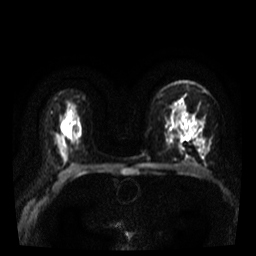
Breast MRI, one axial slice. Diffusion-weighted series; image 2 of 4 stored at this slice position (different b-values; order by instance number). 3 T. 5 mm slice thickness. 256 × 256 image matrix. Female patient.
Annotated regions visible in this slice (manually delineated by an expert):
- tumour on diffusion-weighted imaging: box from (x=181, y=116) to (x=193, y=140) px